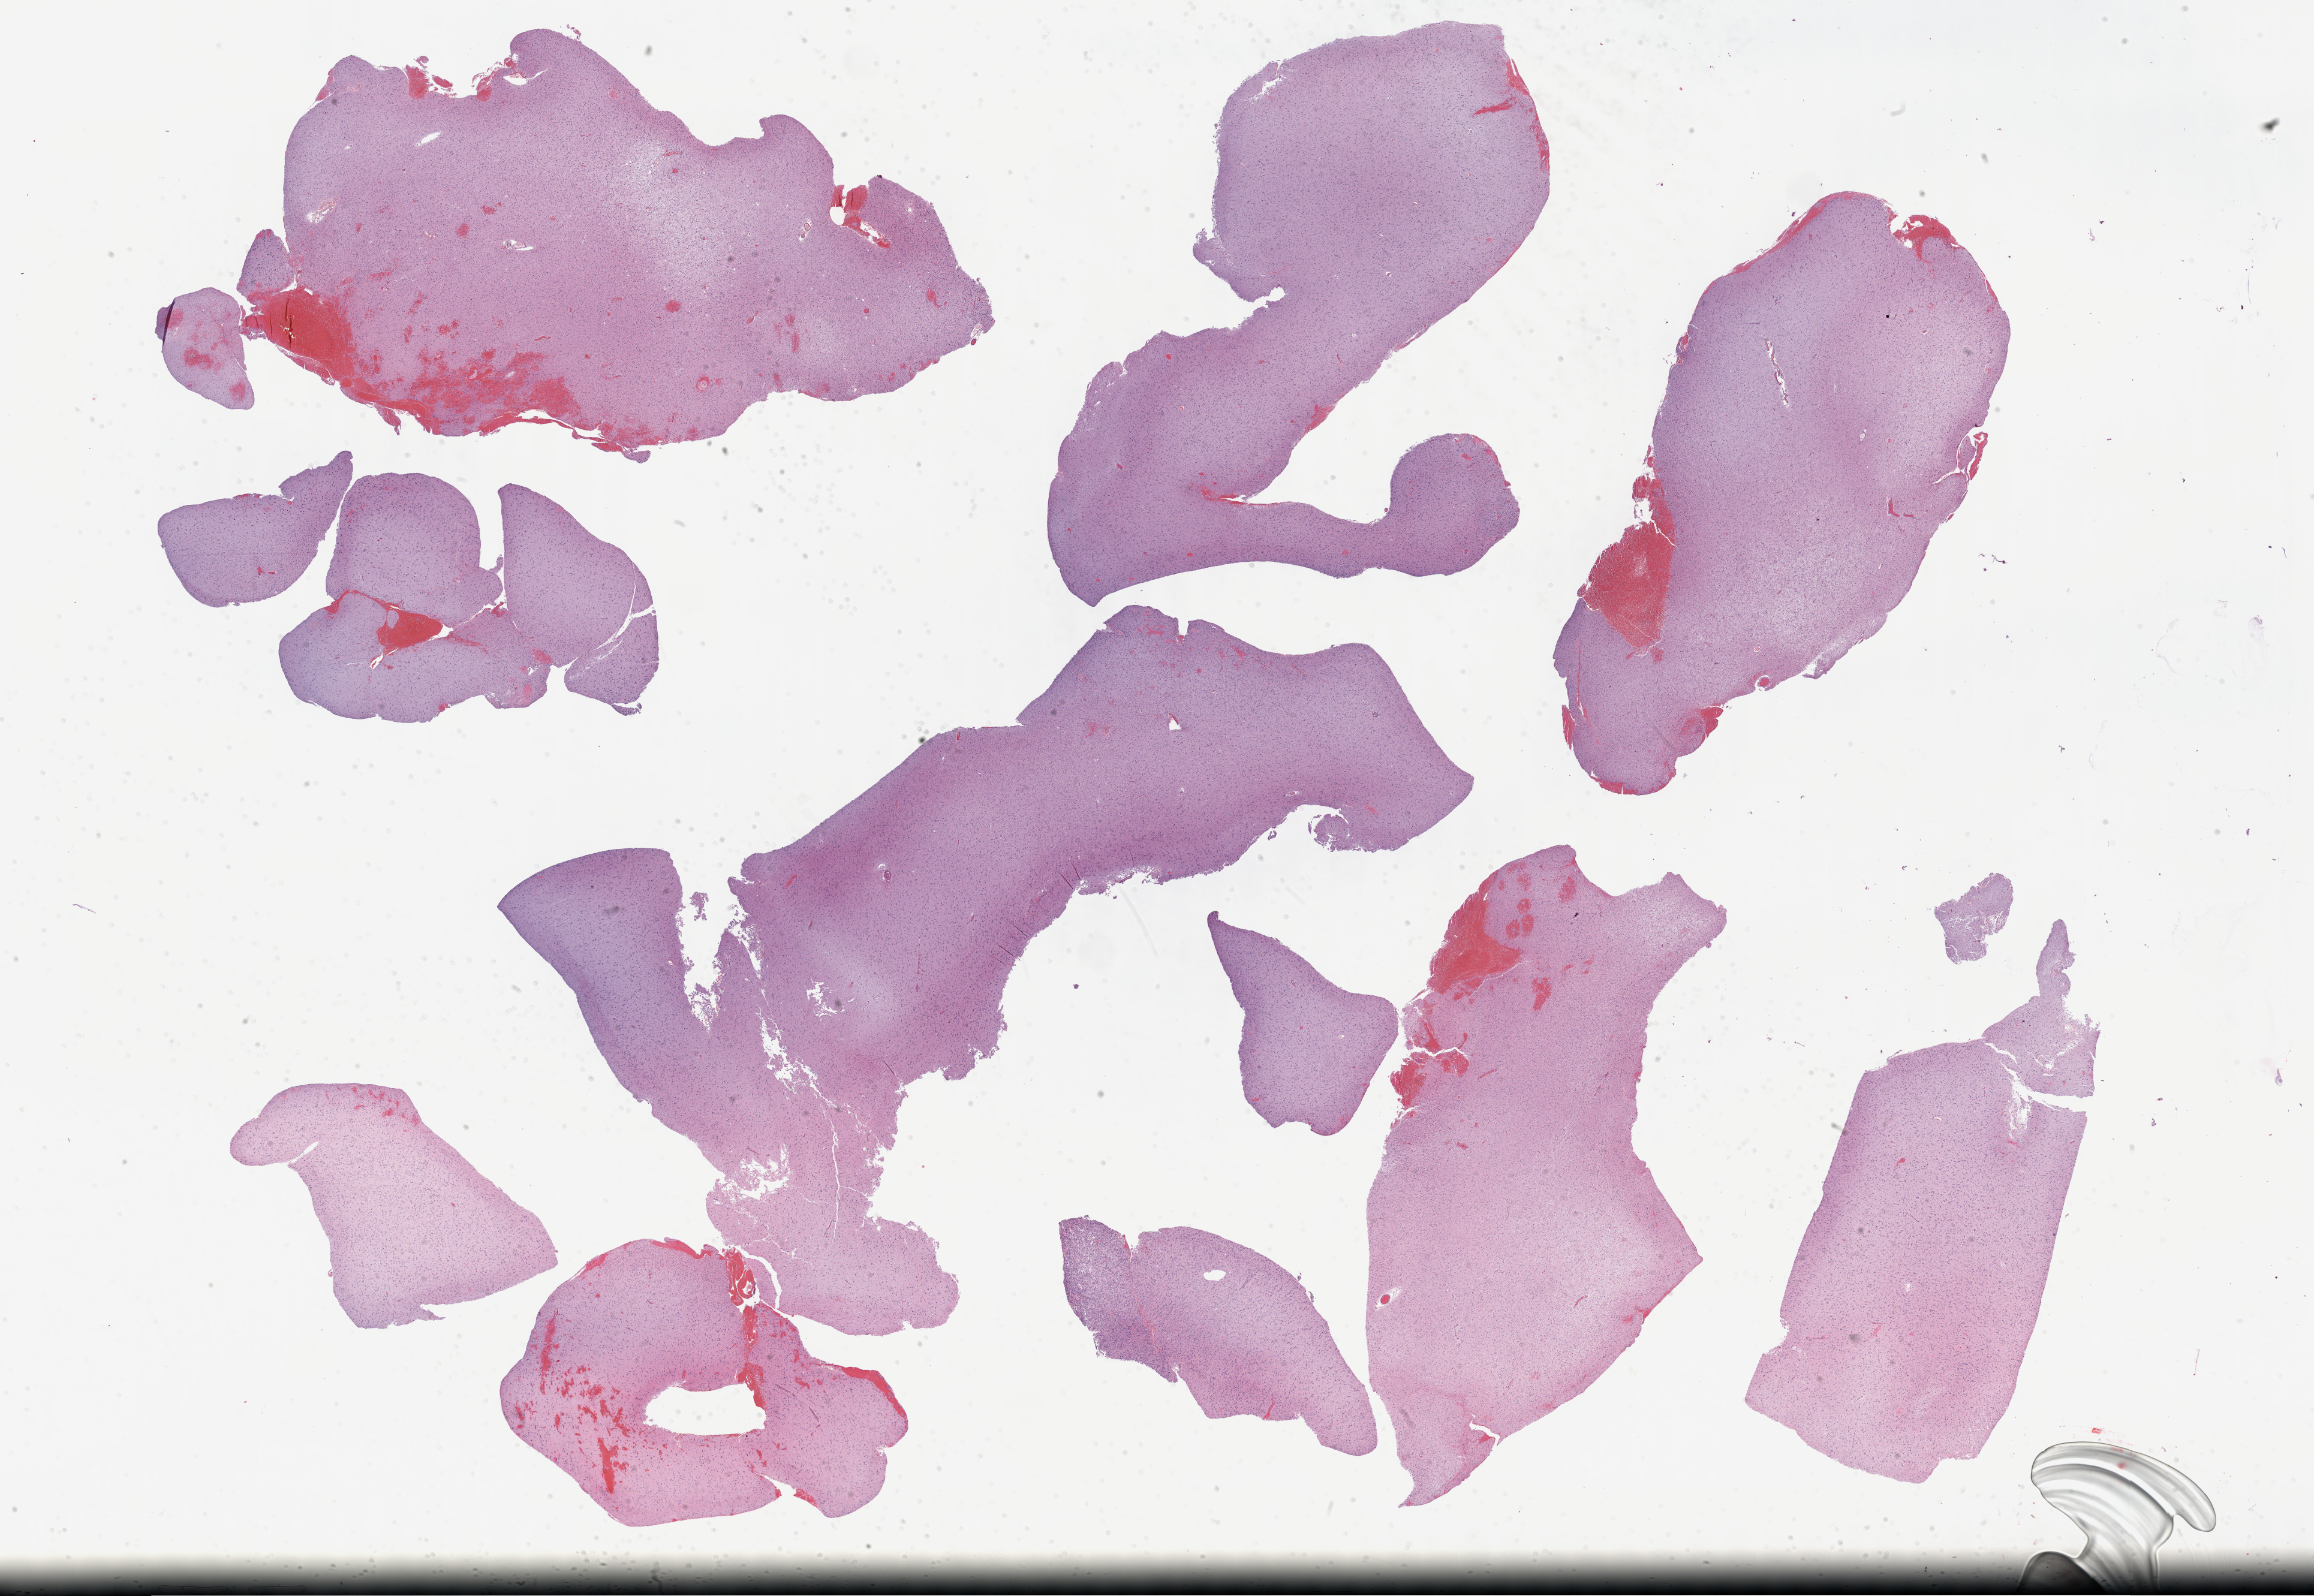
H&E whole-slide image — whole scanned area (about 31.2 x 21.5 mm, acquisition: 40x scan) shown as a low-resolution overview. FFPE section. Brain, primary tumour sample. Male, age 54 years at initial diagnosis. Histologic grade: G2 (moderately differentiated).
Diagnosis: Oligodendroglioma, NOS (cerebrum).